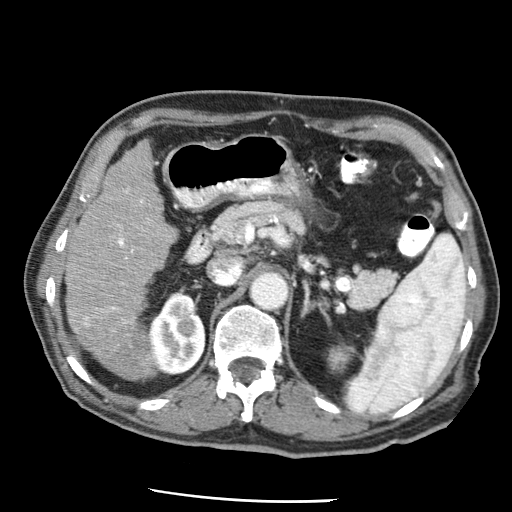
Contrast-enhanced abdominal CT (liver protocol), one axial slice. Soft-tissue window (W 400 / L 40 HU). 2.5 mm slice thickness. 512 × 512 image matrix. Case-level facts recorded for this patient, not image findings: diagnosis: hepatocellular carcinoma (patient treated with transarterial chemoembolisation; whether this scan precedes or follows treatment is not stated here); TNM stage (as recorded): Stage-IIIA; Child-Pugh class: A.
Structures marked on this image (semi-automatic segmentation, software-assisted and operator-edited):
- liver parenchyma outside the tumour (the mass and vessels are separate outlines, so this box may not span the whole liver): bounding box <65,140,176,378> (left, top, right, bottom; pixels)
- liver vessels: <84,189,143,326>